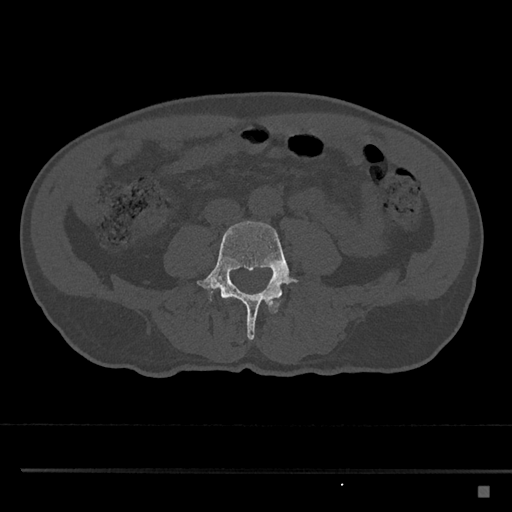
CT including the spine, one axial slice; slice 638 of 797 in the series (ordered by position); reconstruction kernel Br40s/3; 120 kVp; bone window (W 1800 / L 400 HU); 0.5 mm slice thickness; 512 × 512 image matrix, field of view 391 × 391 mm. Patient: male, 59 years. Case-level facts recorded for this patient, not image findings: primary cancer: prostate.
Annotated regions visible in this slice (semi-automatic segmentation, software-assisted and operator-edited):
- L3 vertebra: bounding box (x1, y1, x2, y2) in pixels: (224, 296, 281, 313)
- L4 vertebra: (197, 221, 298, 341)
- L5 vertebra: (205, 288, 213, 302)